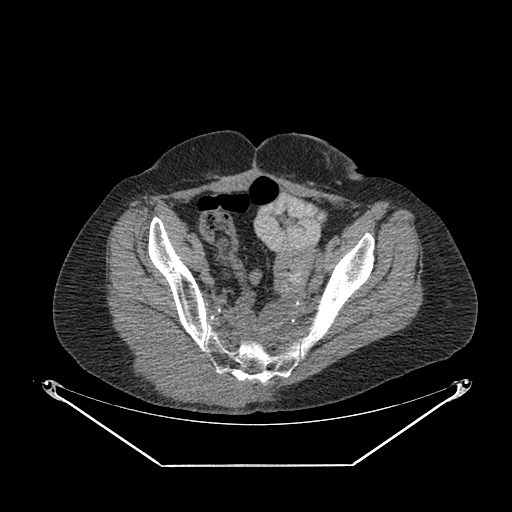
CT of an extremity soft-tissue mass (from a PET/CT study), one axial slice; position 67 of 267 along the scan axis; 140 kVp; soft-tissue window (W 400 / L 40 HU); 3.75 mm slice thickness; 512 × 512 image matrix, field of view 500 × 500 mm. Female patient. Case-level facts recorded for this patient, not image findings: histological type: spindle cell suggestive of myxofibrosarcoma; grade: intermediate; site of the primary tumour: right buttock.
Structures marked on this image (expert contour drawn on MRI and transferred to this co-registered scan by the dataset authors):
- gross tumour volume (mass): box from (x=125, y=331) to (x=250, y=408) px